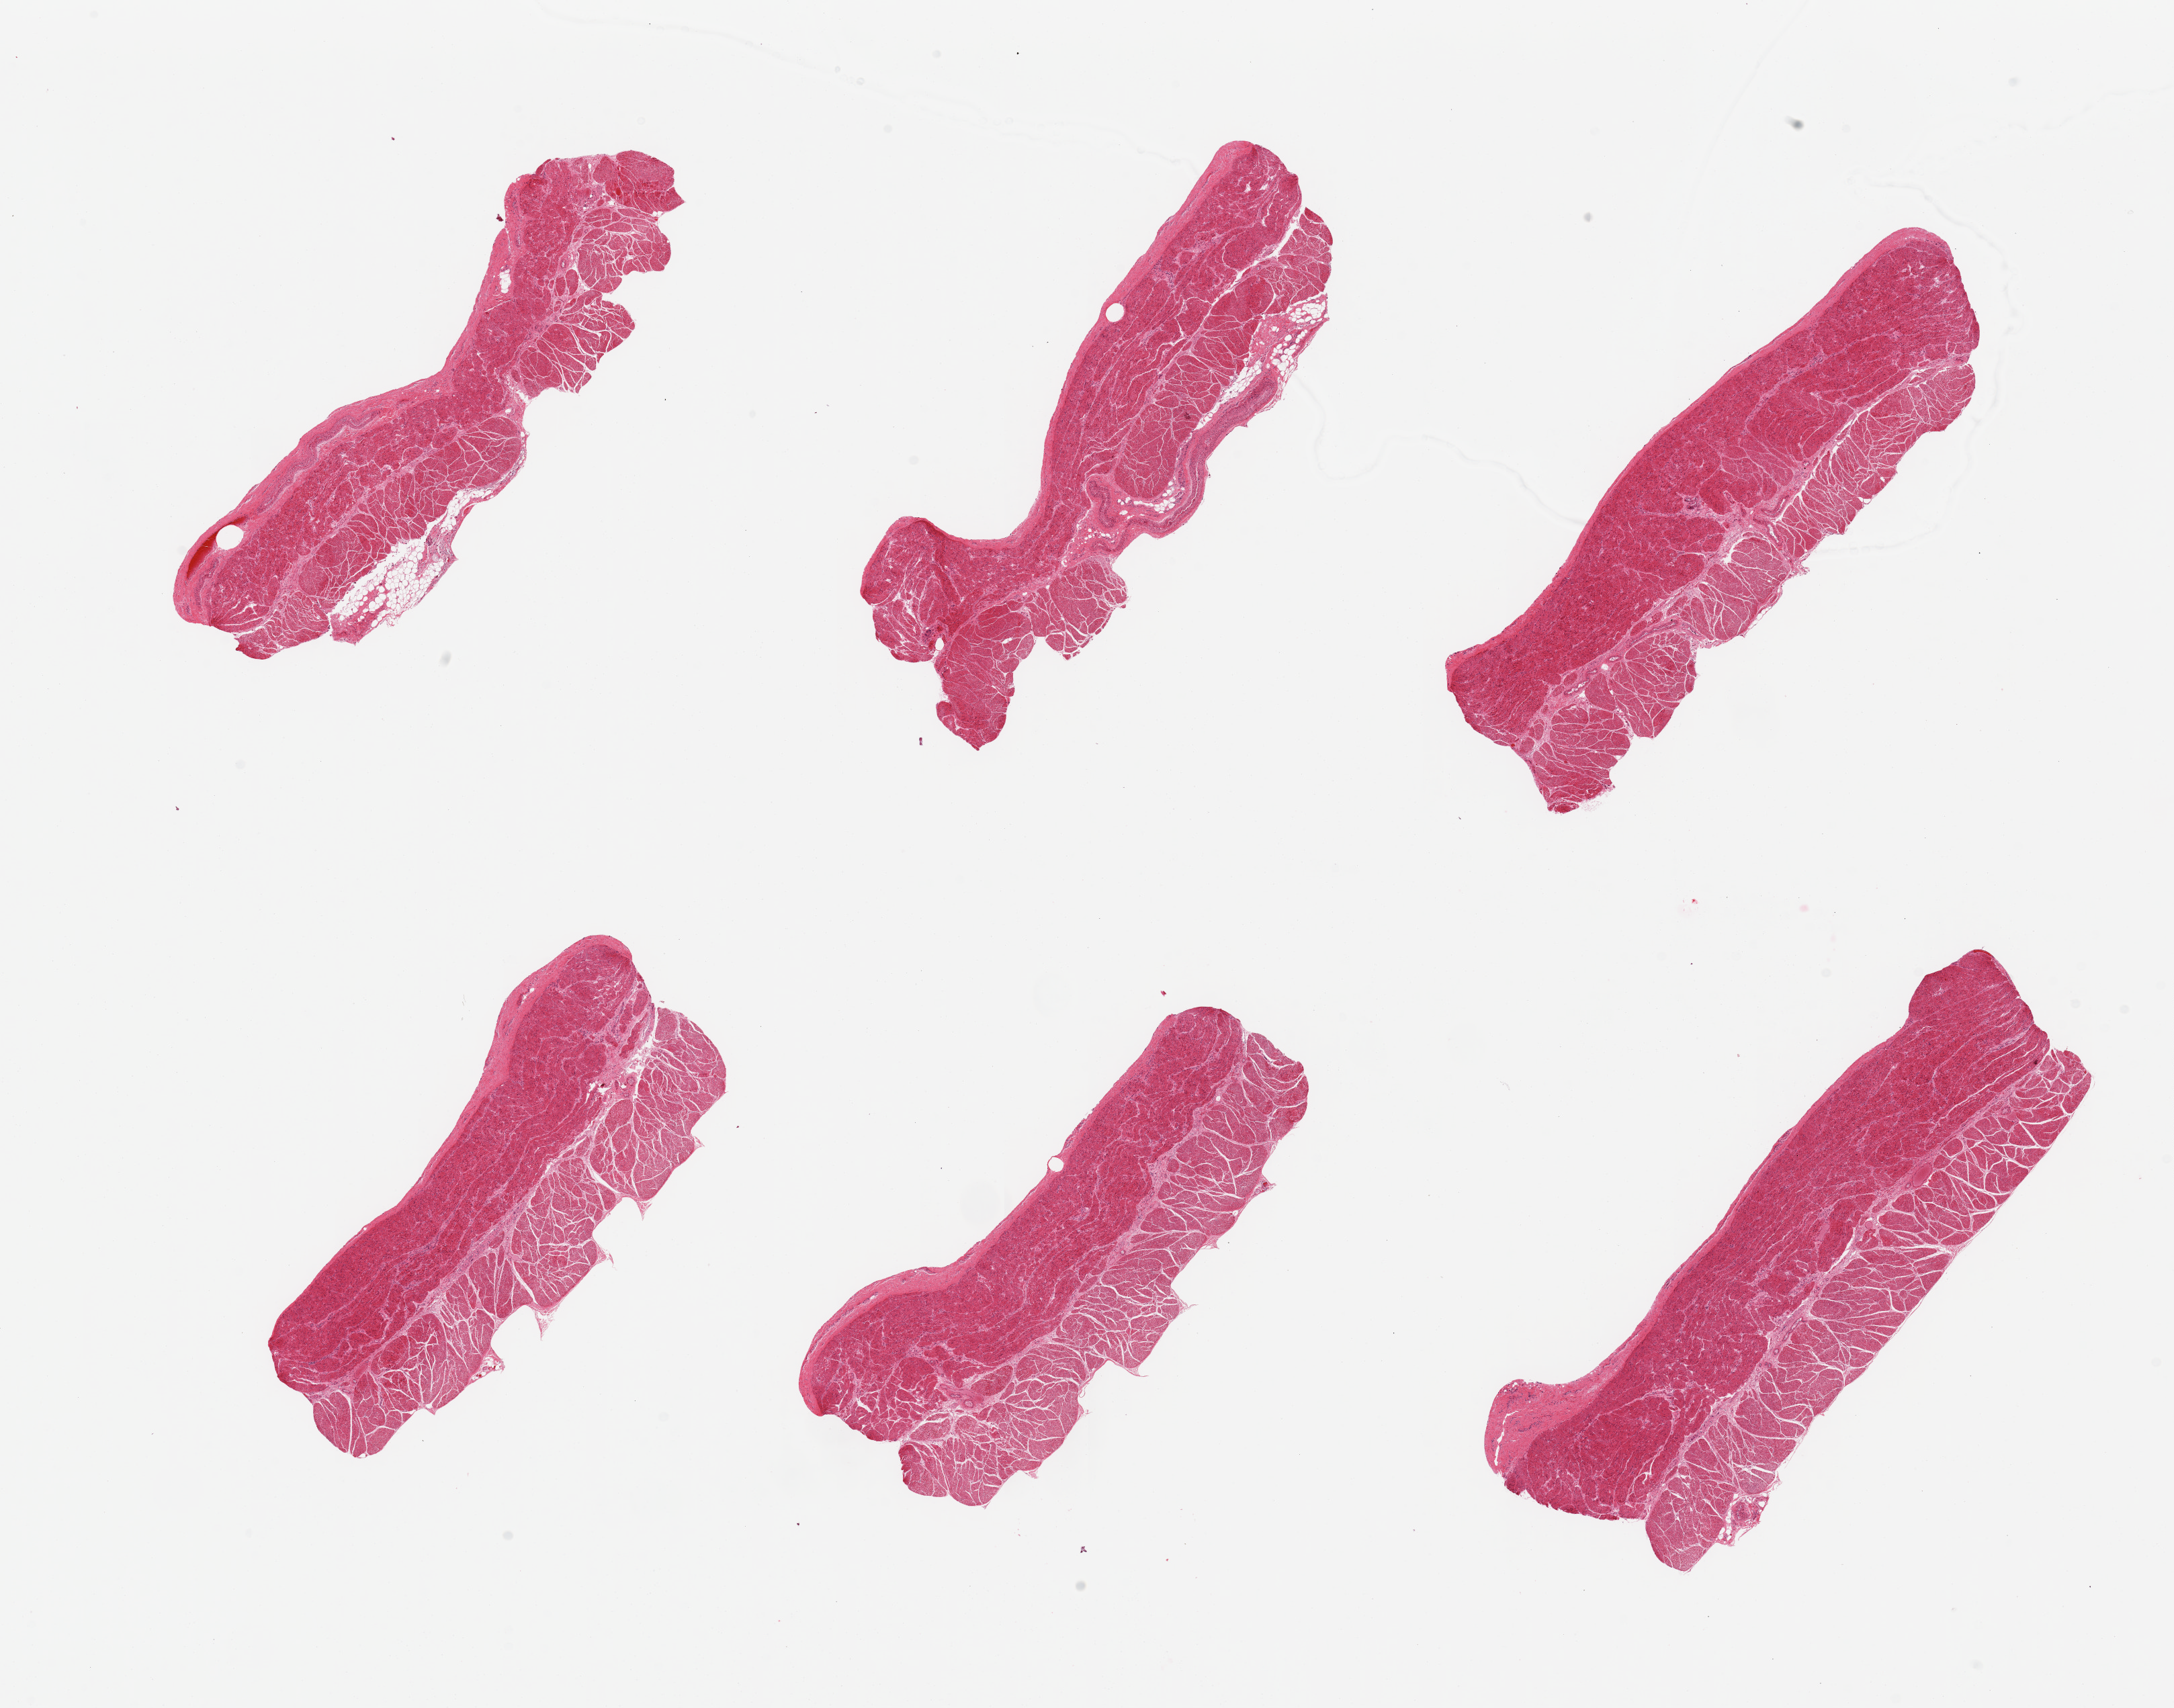
Digitized H&E-stained section — whole scanned area (about 25.6 x 20.1 mm) shown as a low-resolution overview. PAXgene-fixed, paraffin-embedded tissue. Target tissue: gastroesophageal junction. Donor tissue sample. Male donor.
• review note (as recorded): 6 pieces; 5% external fat on 2 pieces